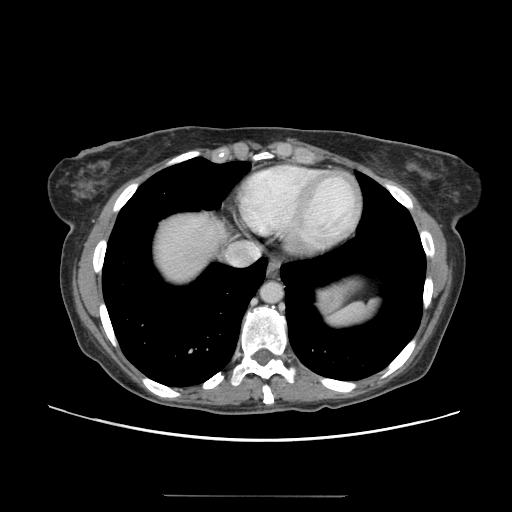
Contrast-enhanced abdominal CT, one axial slice. Position 133 of 144 along the scan axis. Soft-tissue window (W 400 / L 40 HU). 2.5 mm slice thickness. 512 × 512 image matrix. Female patient, age 53 years. From the clinical record (not read from this slice): diagnosis: colorectal cancer liver metastases, imaged before liver resection; multiple liver metastases: yes; largest metastasis: 1.1 cm.
Structures marked on this image (manually delineated by an expert):
- hepatic veins: bounding box (x1, y1, x2, y2) in pixels: (253, 249, 260, 258)
- liver: (153, 211, 222, 282)
- planned liver remnant (the part of the liver to remain after resection): (151, 210, 224, 282)